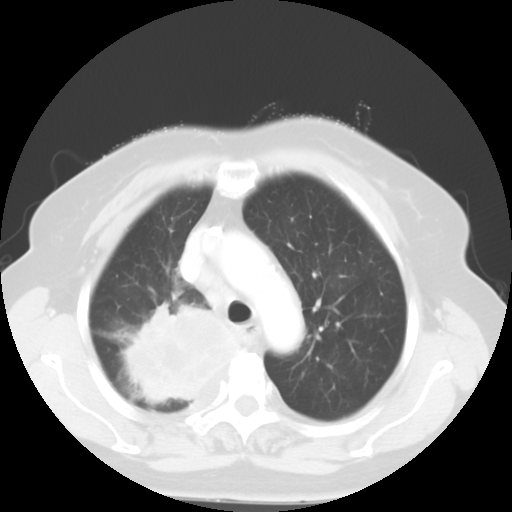
Chest CT, one axial slice. Position 40 of 52 along the scan axis. Reconstruction kernel STANDARD. 120 kVp. Lung window (W 1500 / L -600 HU). 5 mm slice thickness. 512 × 512 image matrix, field of view 333 × 333 mm. Patient: female, 81 years. From the clinical record (not read from this slice): clinical TNM (as recorded): T4 N3 M1b.
Annotated regions visible in this slice (rectangle marked by the reading radiologist):
- lung tumour (recorded histology: adenocarcinoma): box from (x=122, y=301) to (x=242, y=406) px